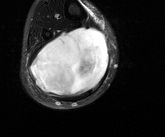
MRI of an extremity soft-tissue mass, one axial slice; T2-weighted fat-saturated; MR volume resampled by the dataset authors to the PET/CT grid (not the native acquisition matrix); 165 × 137 image matrix, field of view 161 × 134 mm. Male patient. Case-level facts recorded for this patient, not image findings: histological type: liposarcoma - round cell; grade: high; site of the primary tumour: right calf.
Outlined on this slice (expert contour drawn on MRI and transferred to this co-registered scan by the dataset authors):
- gross tumour volume (mass): bounding box [x1, y1, x2, y2] px = [32, 27, 109, 97]